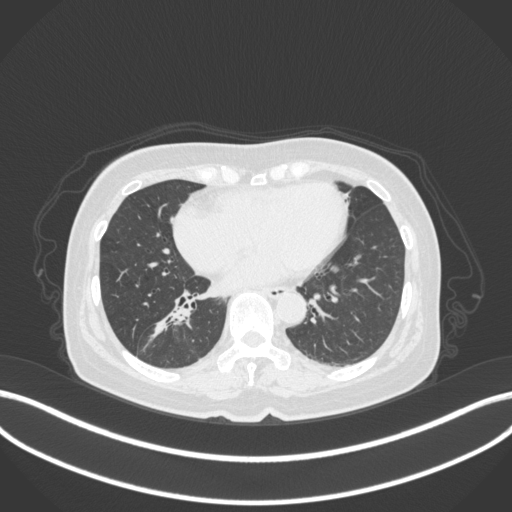
Chest CT, one axial slice; slice 155 of 429 in the series (ordered by position); reconstruction kernel B31f; lung window (W 1500 / L -600 HU); 1 mm slice thickness; 512 × 512 image matrix. Patient: female, 67 years. Case-level facts recorded for this patient, not image findings: clinical TNM (as recorded): T1c N1 M0; histopathological grade: G2-3.
Annotated regions visible in this slice (rectangle marked by the reading radiologist):
- lung tumour (recorded histology: adenocarcinoma): bounding box (x1, y1, x2, y2) in pixels: (145, 293, 194, 341)